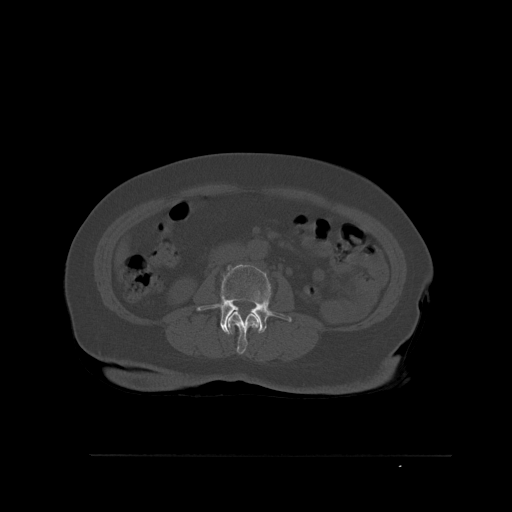
CT including the spine, one axial slice; position 233 of 527 along the scan axis; bone window (W 1800 / L 400 HU); 1.5 mm slice thickness; 512 × 512 image matrix, field of view 470 × 470 mm. Patient: female, 73 years. From the clinical record (not read from this slice): primary cancer: breast; vertebrae with lytic lesions (as recorded): L2.
Outlined on this slice (semi-automatically segmented with operator editing):
- L2 vertebra: bounding box [x1, y1, x2, y2] px = [227, 311, 257, 355]
- L3 vertebra: [197, 264, 292, 335]
- L4 vertebra: [253, 319, 259, 331]